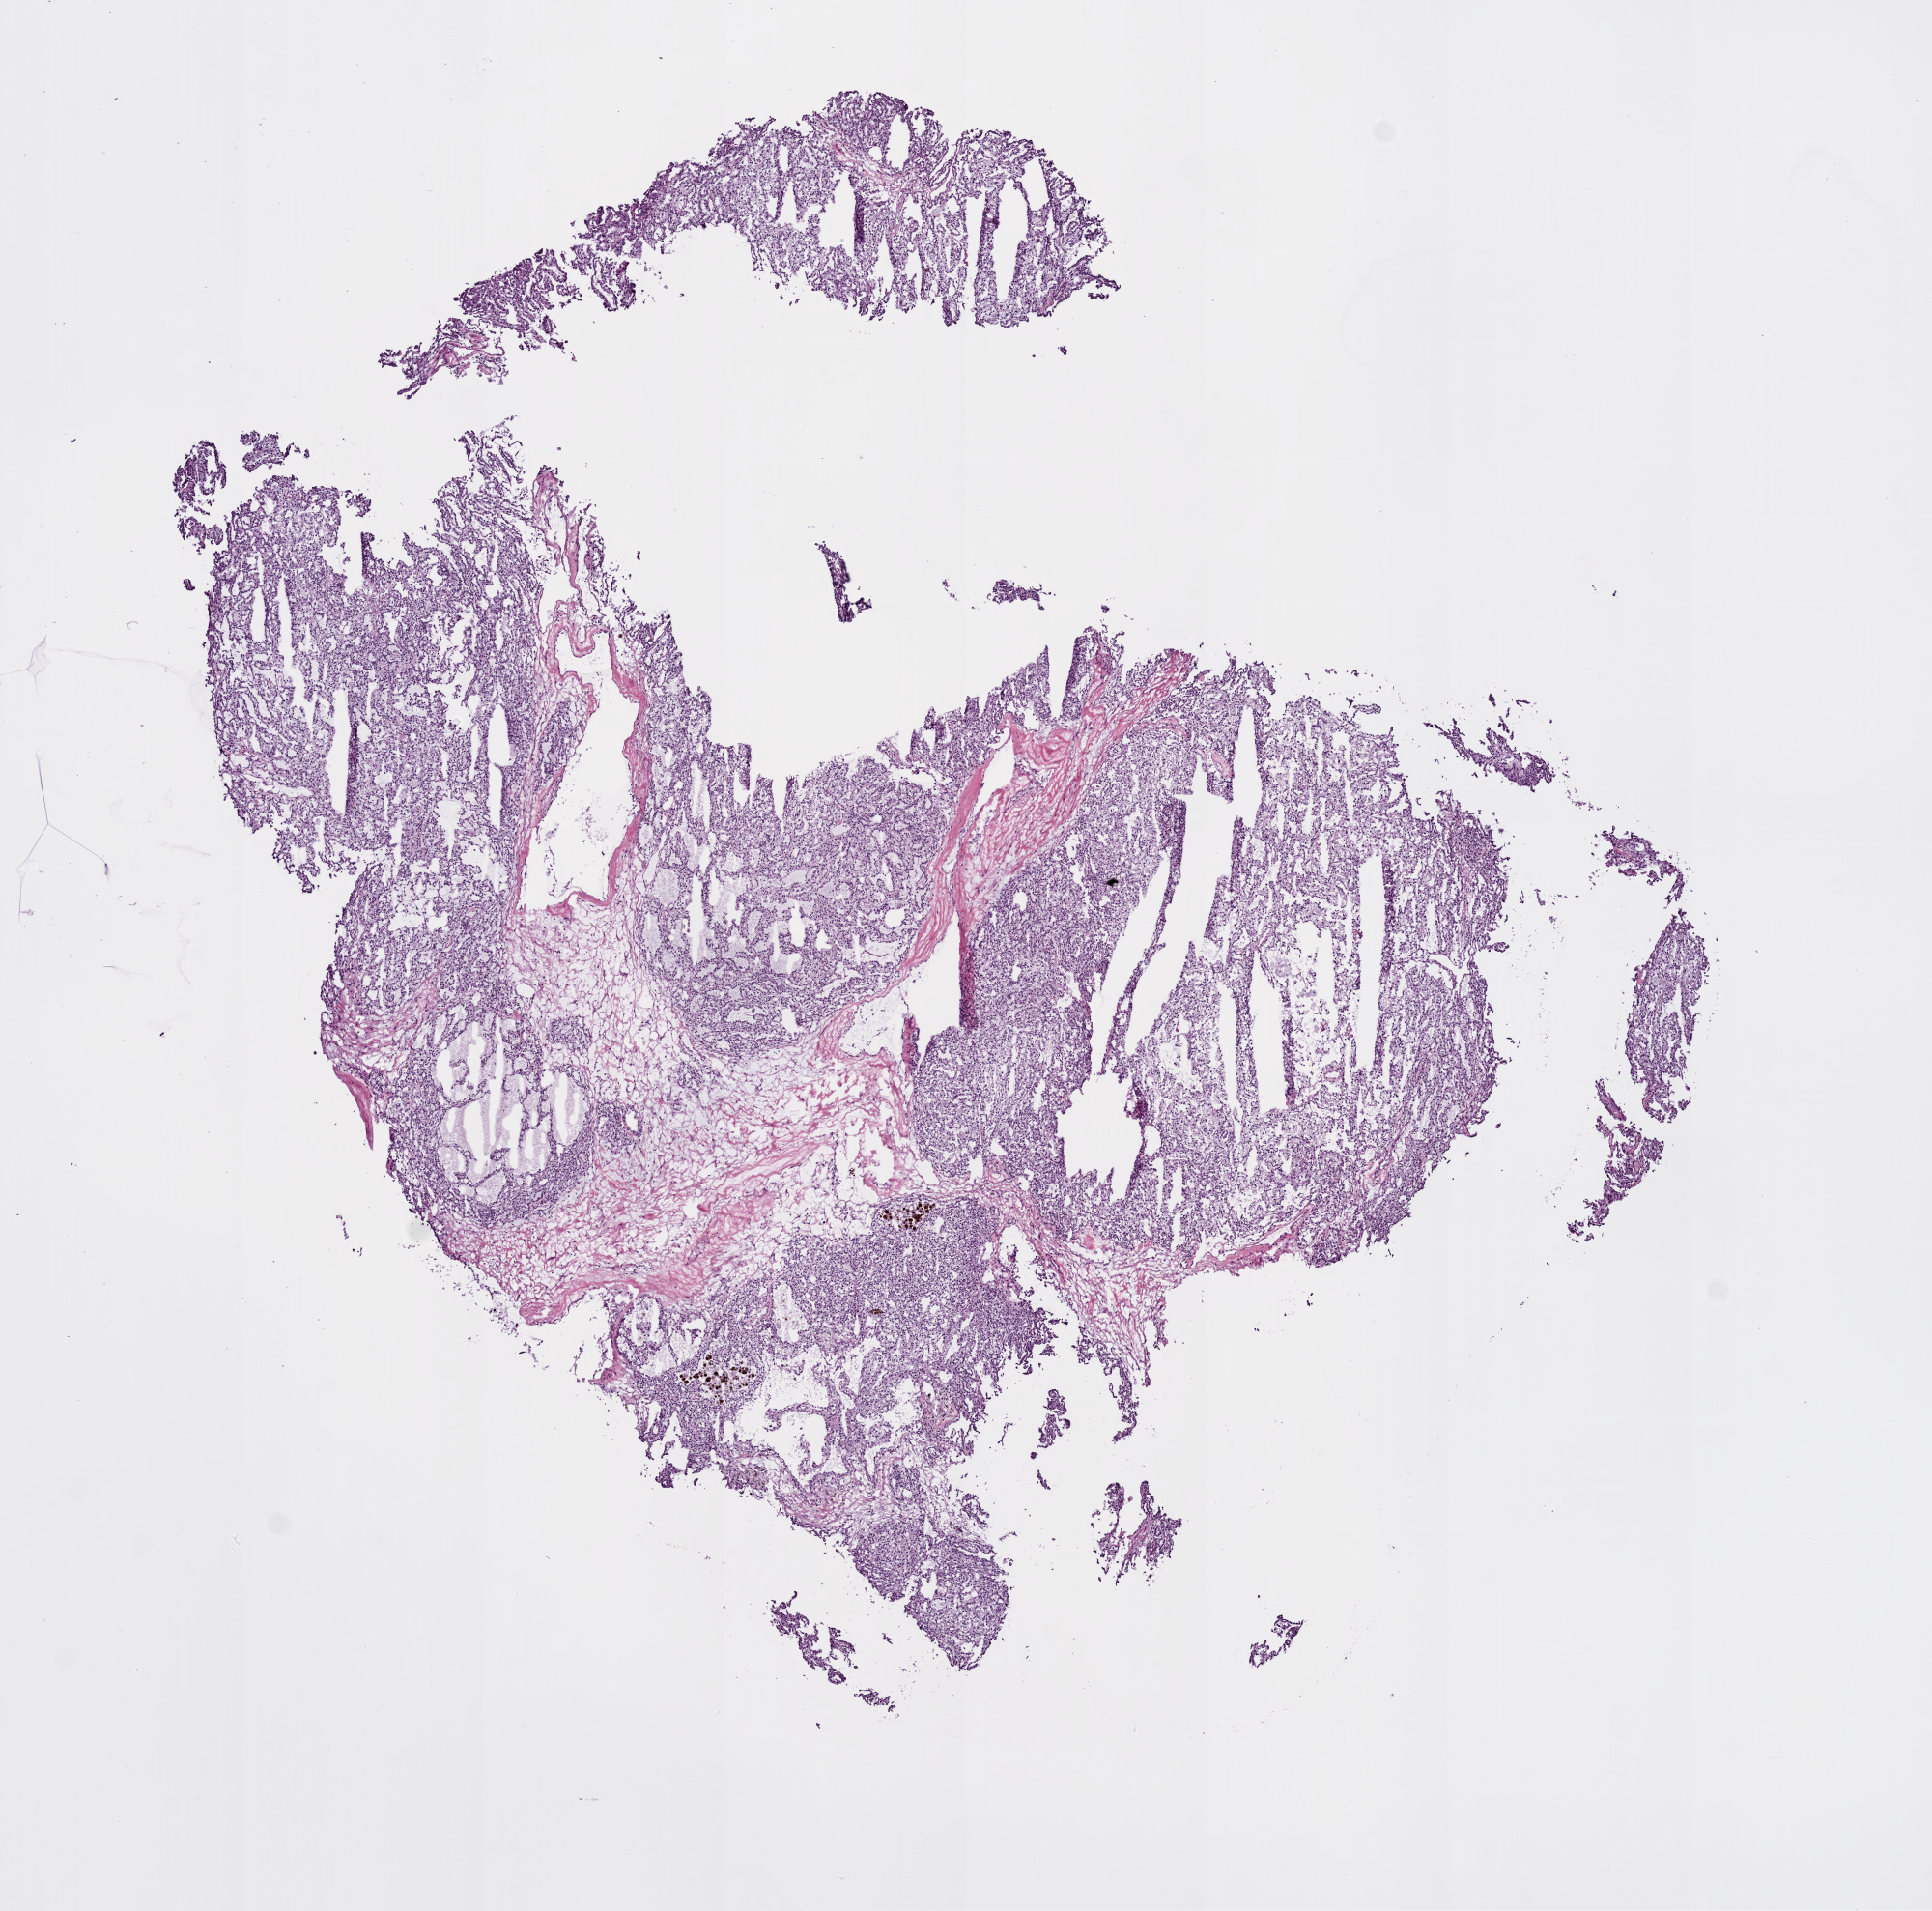
H&E whole-slide image, shown as a low-resolution overview of the whole scanned area (about 8.0 x 7.9 mm, from a 20x scan); frozen section from the bottom of the tissue portion; sample: primary tumour, kidney. Female patient; age at initial diagnosis 40 years. Histologic grade: G2 (moderately differentiated). Composition of this section per pathologist review: tumour cells 85%, tumour nuclei 85%, normal cells 0%, stromal cells 15%, necrosis 0%.
AJCC pathologic stage: I. Histologic diagnosis: Clear cell adenocarcinoma, NOS.